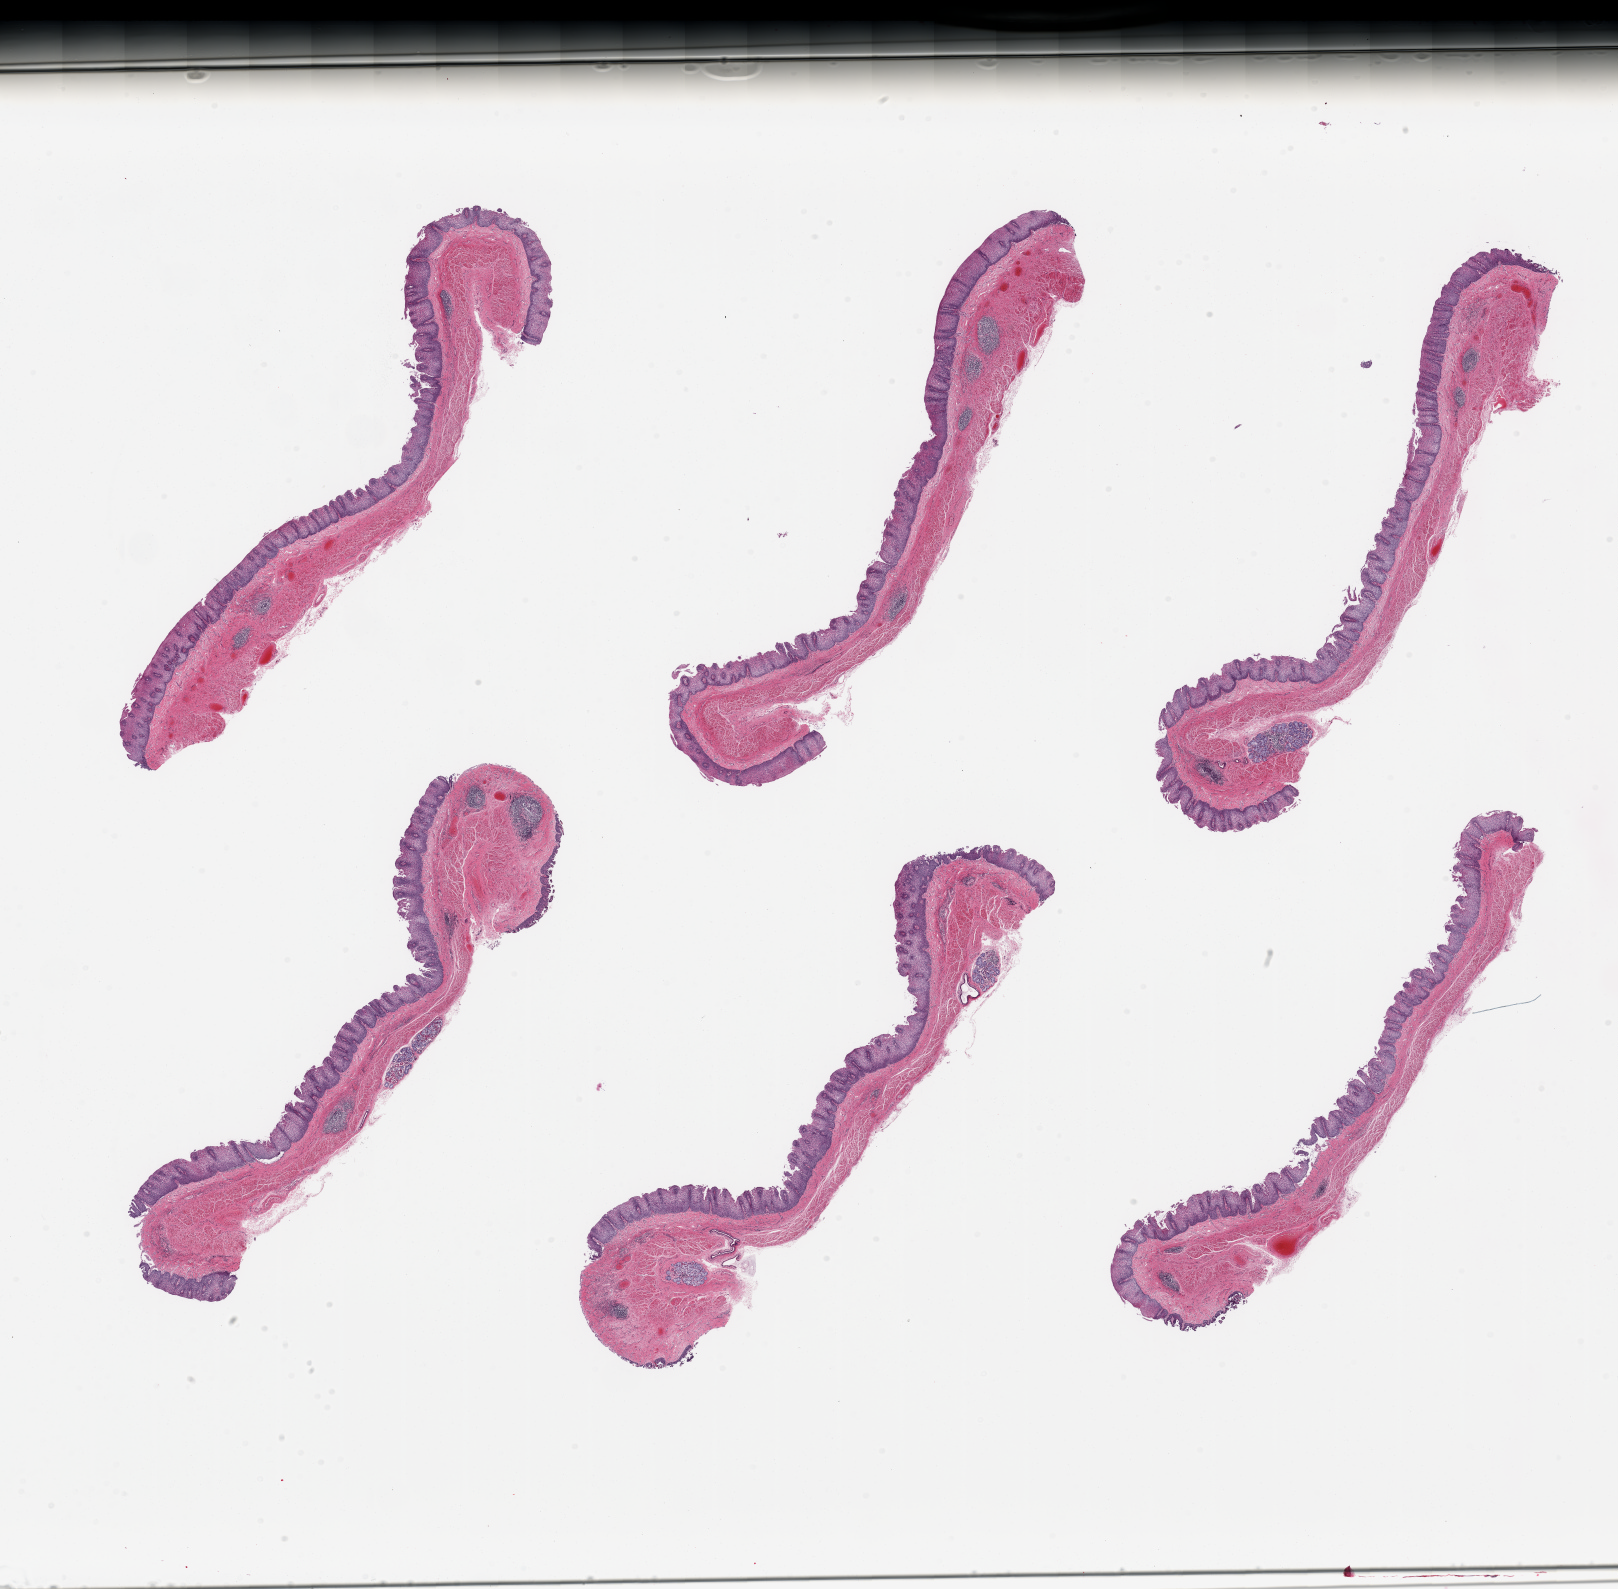
Digitized hematoxylin and eosin (H&E)-stained section, brightfield — a low-resolution overview of the entire scanned area, about 25.6 x 25.1 mm, PAXgene-fixed paraffin-embedded (PFPE) section, target tissue: esophageal mucous membrane, donor tissue sample.
• reviewer comment on this tissue sample: 6 pieces, squamous mucosa up to ~0.3mm, ~20-25% of thickness; Submucosal mucus glands present